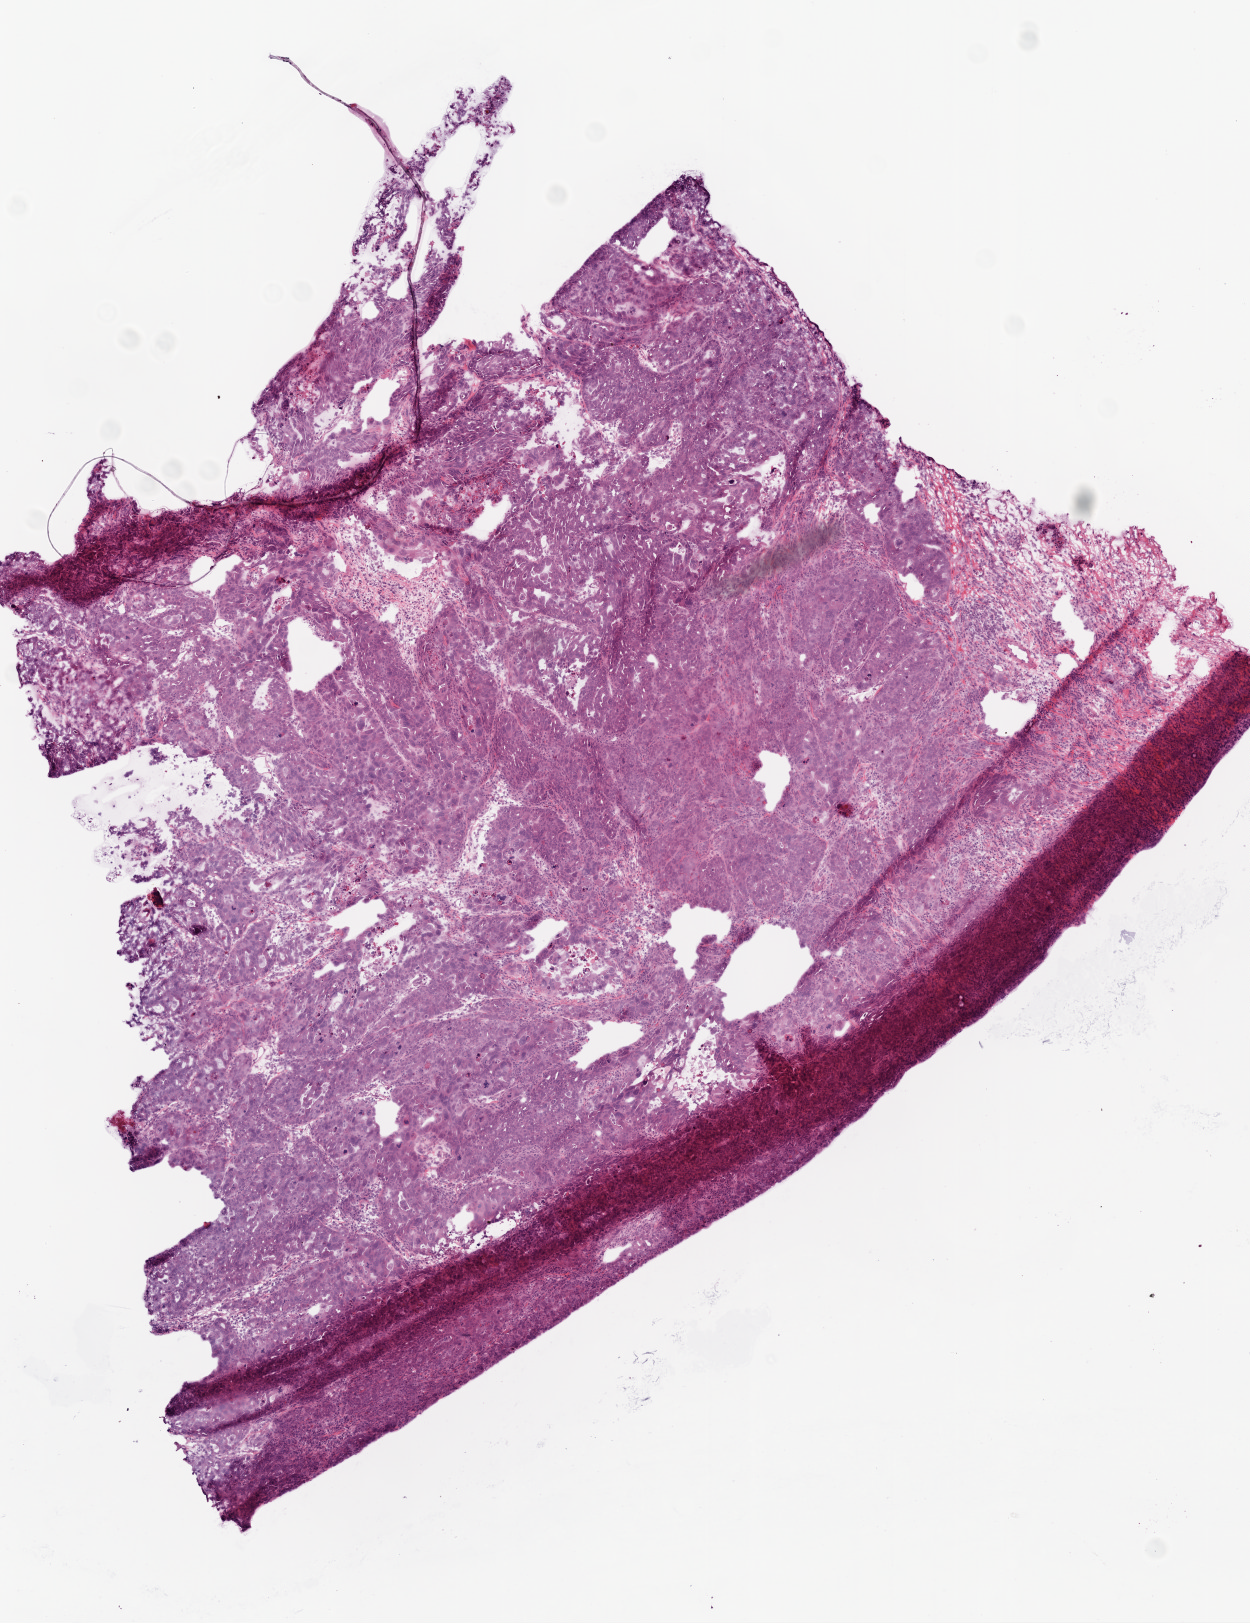
Whole-slide histology image, H&E-stained, low-resolution overview of the scanned area, about 5.0 x 6.5 mm (slide scanned at 20x); frozen section; sample: primary tumour, ovary. Female, age 63 years at initial diagnosis. Histologic grade: G3 (poorly differentiated). Slide review estimates, as recorded: tumour cells 95%, tumour nuclei 95%, normal cells 0%, stromal cells 3%, necrosis 2%.
• FIGO stage: IIC
• pathologic diagnosis: Serous cystadenocarcinoma, NOS